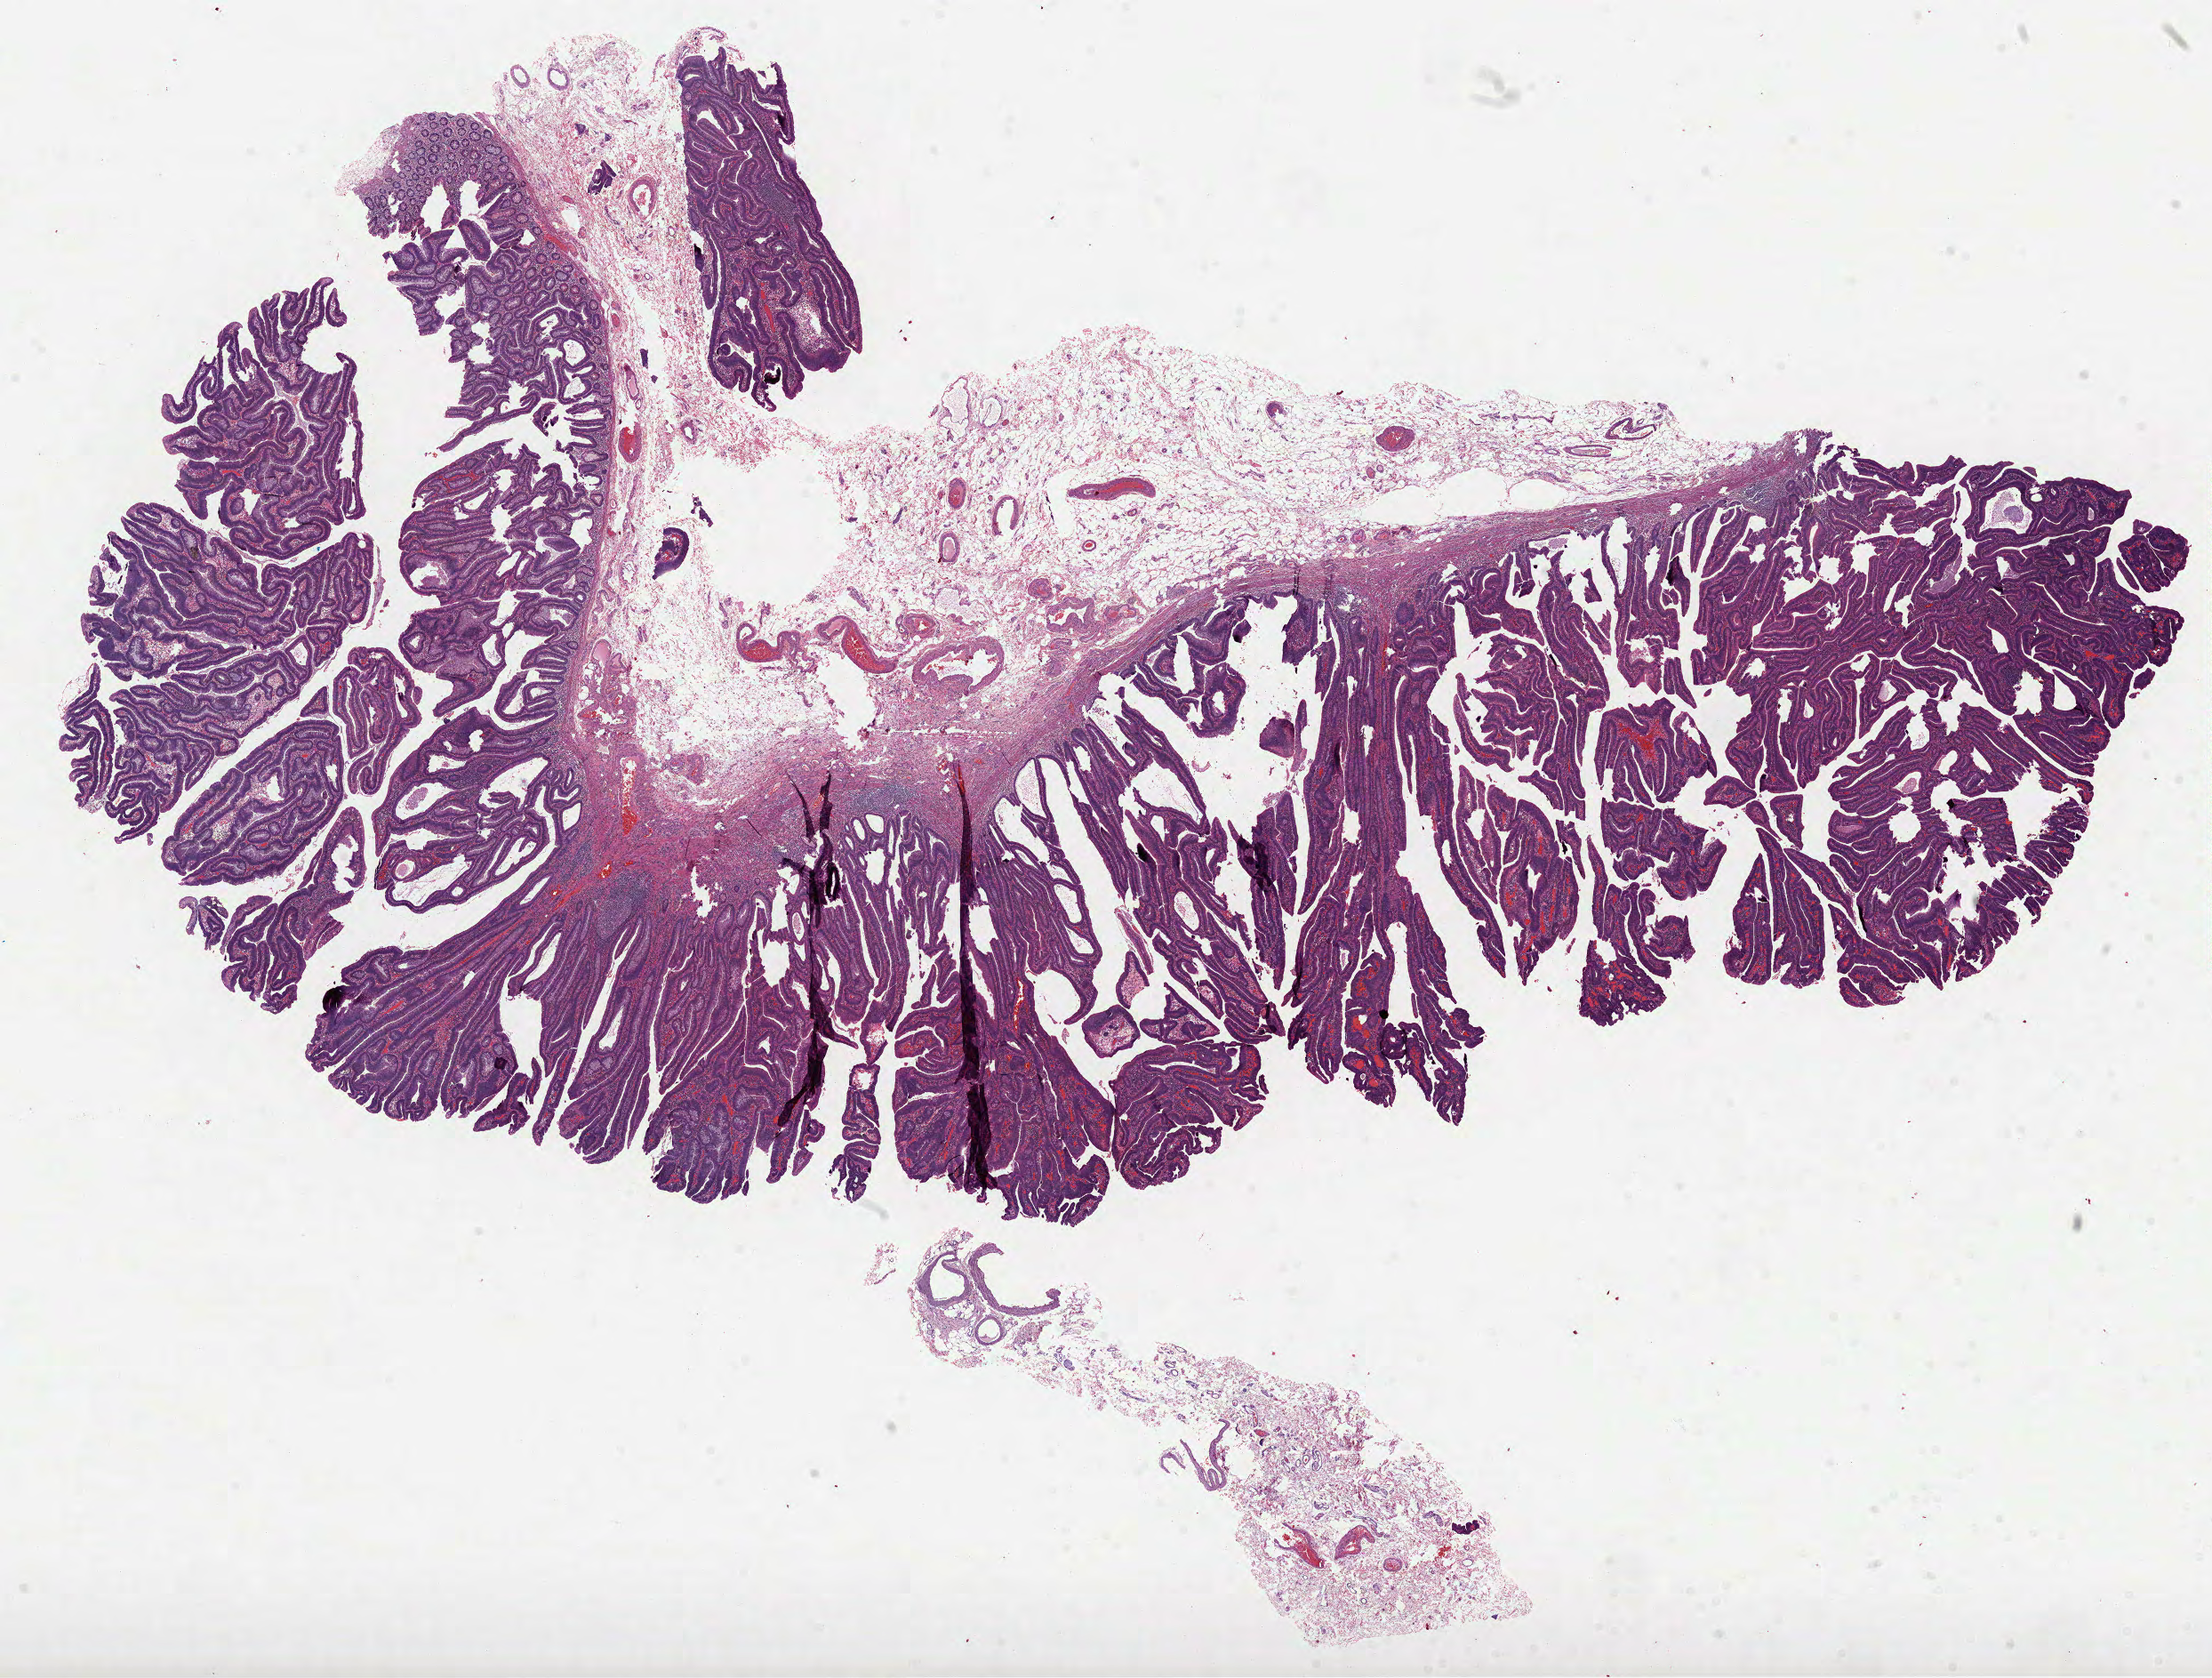
Whole-slide histology image, H&E-stained, whole scanned area (about 20.1 x 15.2 mm) shown as a low-resolution overview. Formalin-fixed paraffin-embedded (FFPE) diagnostic section. Sample: primary tumour, colon. Patient: female, age at initial diagnosis 51 years.
Diagnosis: Adenocarcinoma, NOS (cecum). Lymph nodes positive (case pathology): 0 of 16 examined. AJCC pathologic stage: I.